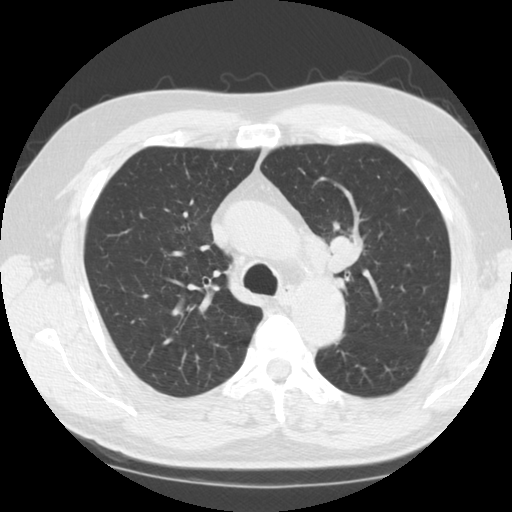
Low-dose screening chest CT, one axial slice. Slice 89 of 124 in the series (ordered by position). Lung window (W 1500 / L -600 HU). 512 × 512 image matrix.
Outlined on this slice (outlined manually by an expert reader):
- lesion 1 (tumor, upper lobe of left lung): bounding box [x1, y1, x2, y2] px = [329, 229, 362, 272]